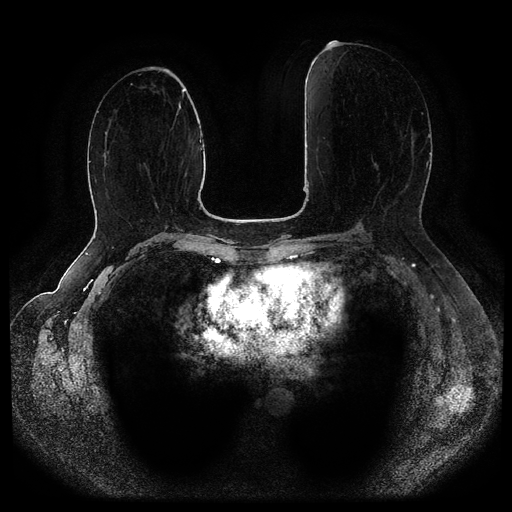
Breast MRI (dynamic contrast-enhanced, multi-phase), one axial slice. Slice 47 of 116 in the series (ordered by position). Dynamic contrast-enhanced series, time point 2 of 5 at this slice position (early post-contrast). 1.5 T. TE 2.6 ms, TR 5.3 ms. 2 mm slice thickness. 512 × 512 image matrix, field of view 360 × 360 mm. Female patient, age 55 years.
Outlined on this slice (semi-automatic segmentation, software-assisted and operator-edited):
- breast lesion (labelled benign in the annotation): bounding box <375,163,378,167> (left, top, right, bottom; pixels)